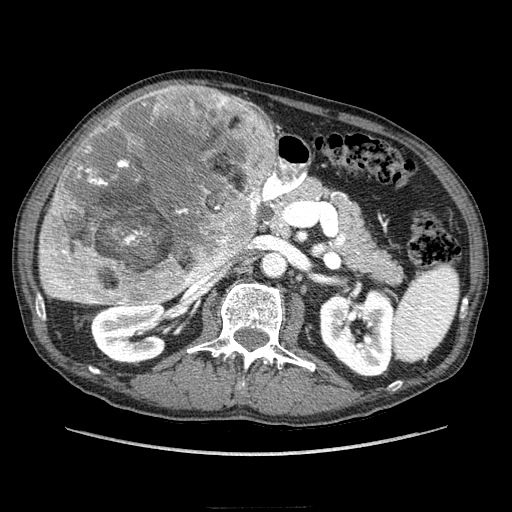
Contrast-enhanced abdominal CT (liver protocol), one axial slice; slice 117 of 218 in the series (ordered by position); reconstruction kernel STANDARD; soft-tissue window (W 400 / L 40 HU); 2.5 mm slice thickness; 512 × 512 image matrix, field of view 380 × 380 mm. From the clinical record (not read from this slice): diagnosis: hepatocellular carcinoma (patient treated with transarterial chemoembolisation; whether this scan precedes or follows treatment is not stated here); TNM stage (as recorded): Stage-IIIA; Child-Pugh class: A; tumour nodularity: multinodular.
Outlined on this slice (semi-automatically segmented with operator editing):
- liver parenchyma outside the tumour (the mass and vessels are separate outlines, so this box may not span the whole liver): bounding box <38,127,276,304> (left, top, right, bottom; pixels)
- mass: <44,82,276,306>
- liver vessels: <42,250,93,303>